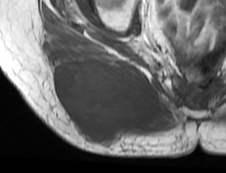
MRI of an extremity soft-tissue mass, one axial slice. Slice 34 of 73 in the series (ordered by position). MR volume resampled by the dataset authors to the PET/CT grid (not the native acquisition matrix). 3.27 mm slice thickness. 226 × 173 image matrix, field of view 221 × 169 mm. Female patient. Case-level facts recorded for this patient, not image findings: histological type: spindle cell suggestive of myxofibrosarcoma; grade: intermediate; site of the primary tumour: right buttock.
Structures marked on this image (expert contour drawn on MRI and transferred to this co-registered scan by the dataset authors):
- gross tumour volume (mass): box from (x=49, y=47) to (x=160, y=146) px